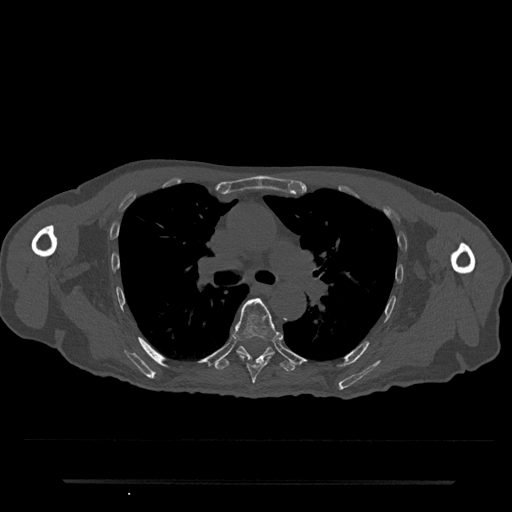
CT including the spine, one axial slice; position 512 of 797 along the scan axis; reconstruction kernel Br40s/3; 120 kVp; bone window (W 1800 / L 400 HU); 0.5 mm slice thickness; 512 × 512 image matrix, field of view 427 × 427 mm. Patient: male, 74 years. From the clinical record (not read from this slice): primary cancer: prostate.
Outlined on this slice (semi-automatic segmentation, software-assisted and operator-edited):
- T6 vertebra: bounding box [x1, y1, x2, y2] px = [233, 298, 280, 385]
- T7 vertebra: [216, 346, 295, 371]